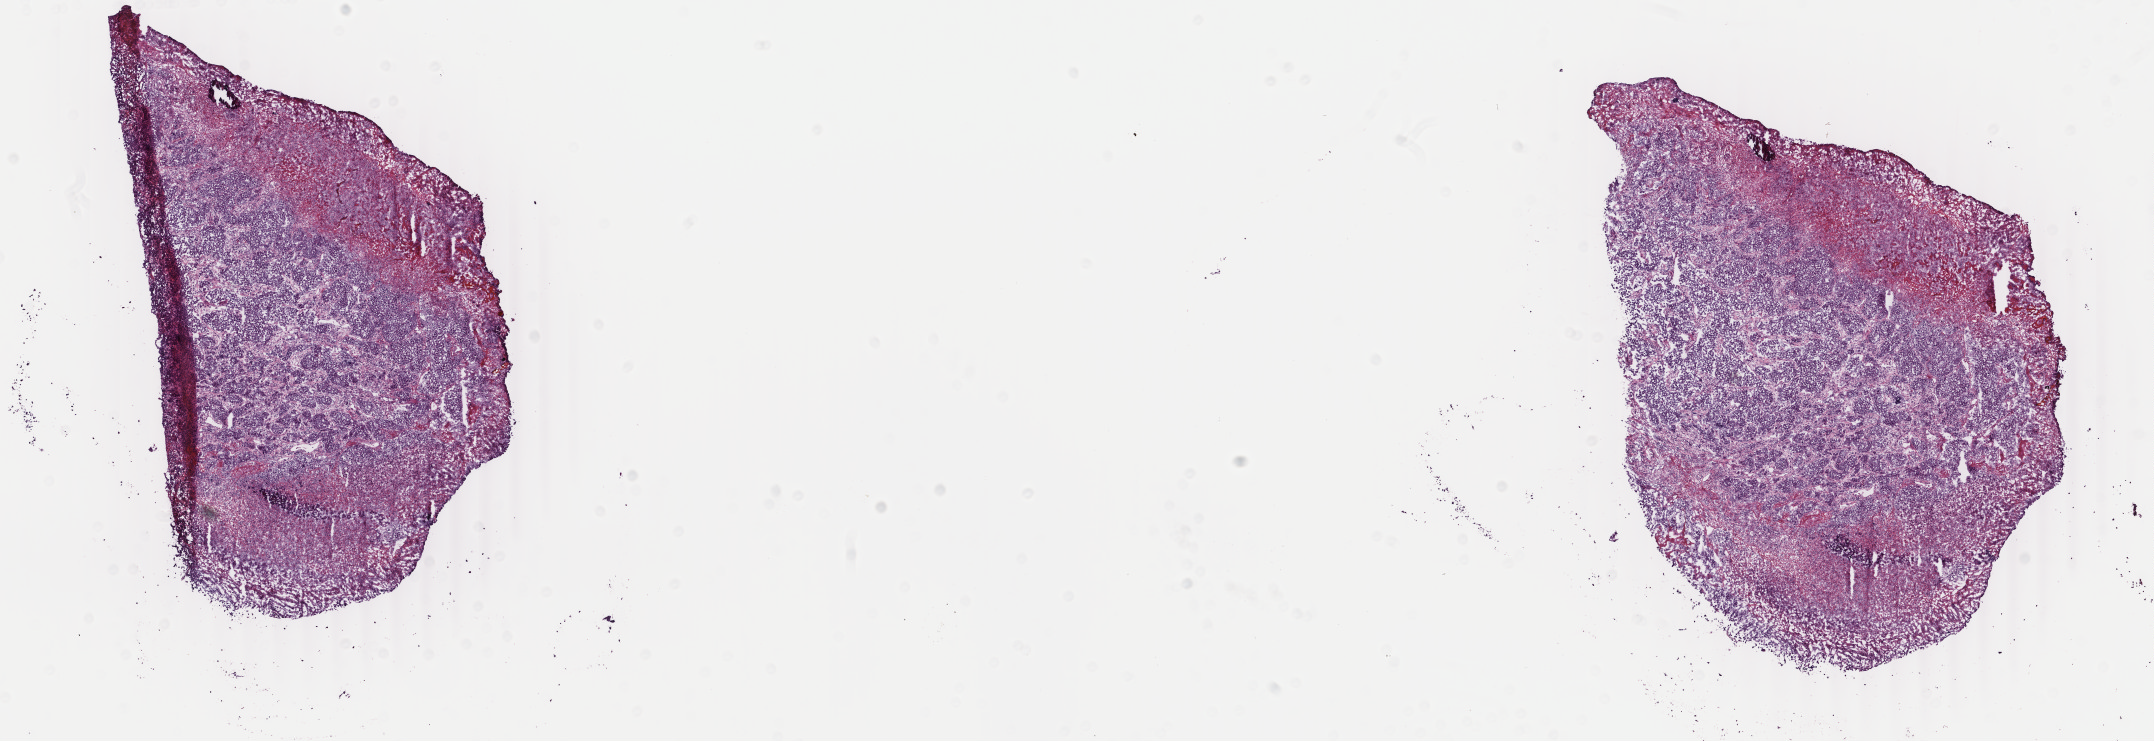
Digitized Hematoxylin and eosin (H&E) stained tissue section (whole slide), low-resolution overview of the scanned area, about 17.1 x 5.9 mm (from a 40x scan), frozen section from the top of the tissue portion, sample: primary tumour, bladder. Patient: male, age at initial diagnosis 83 years. Histologic grade: high grade. Pathologist review of this section (percent, as recorded): tumour cells 73%, tumour nuclei 73%, normal cells 0%, stromal cells 2%, necrosis 25%. Inflammatory infiltration, as recorded: lymphocyte infiltration 0%, monocyte infiltration 0%, neutrophil infiltration 0%.
* histologic diagnosis: Transitional cell carcinoma
* lymph nodes positive (case pathology): 4 of 11 examined
* AJCC pathologic stage: IV